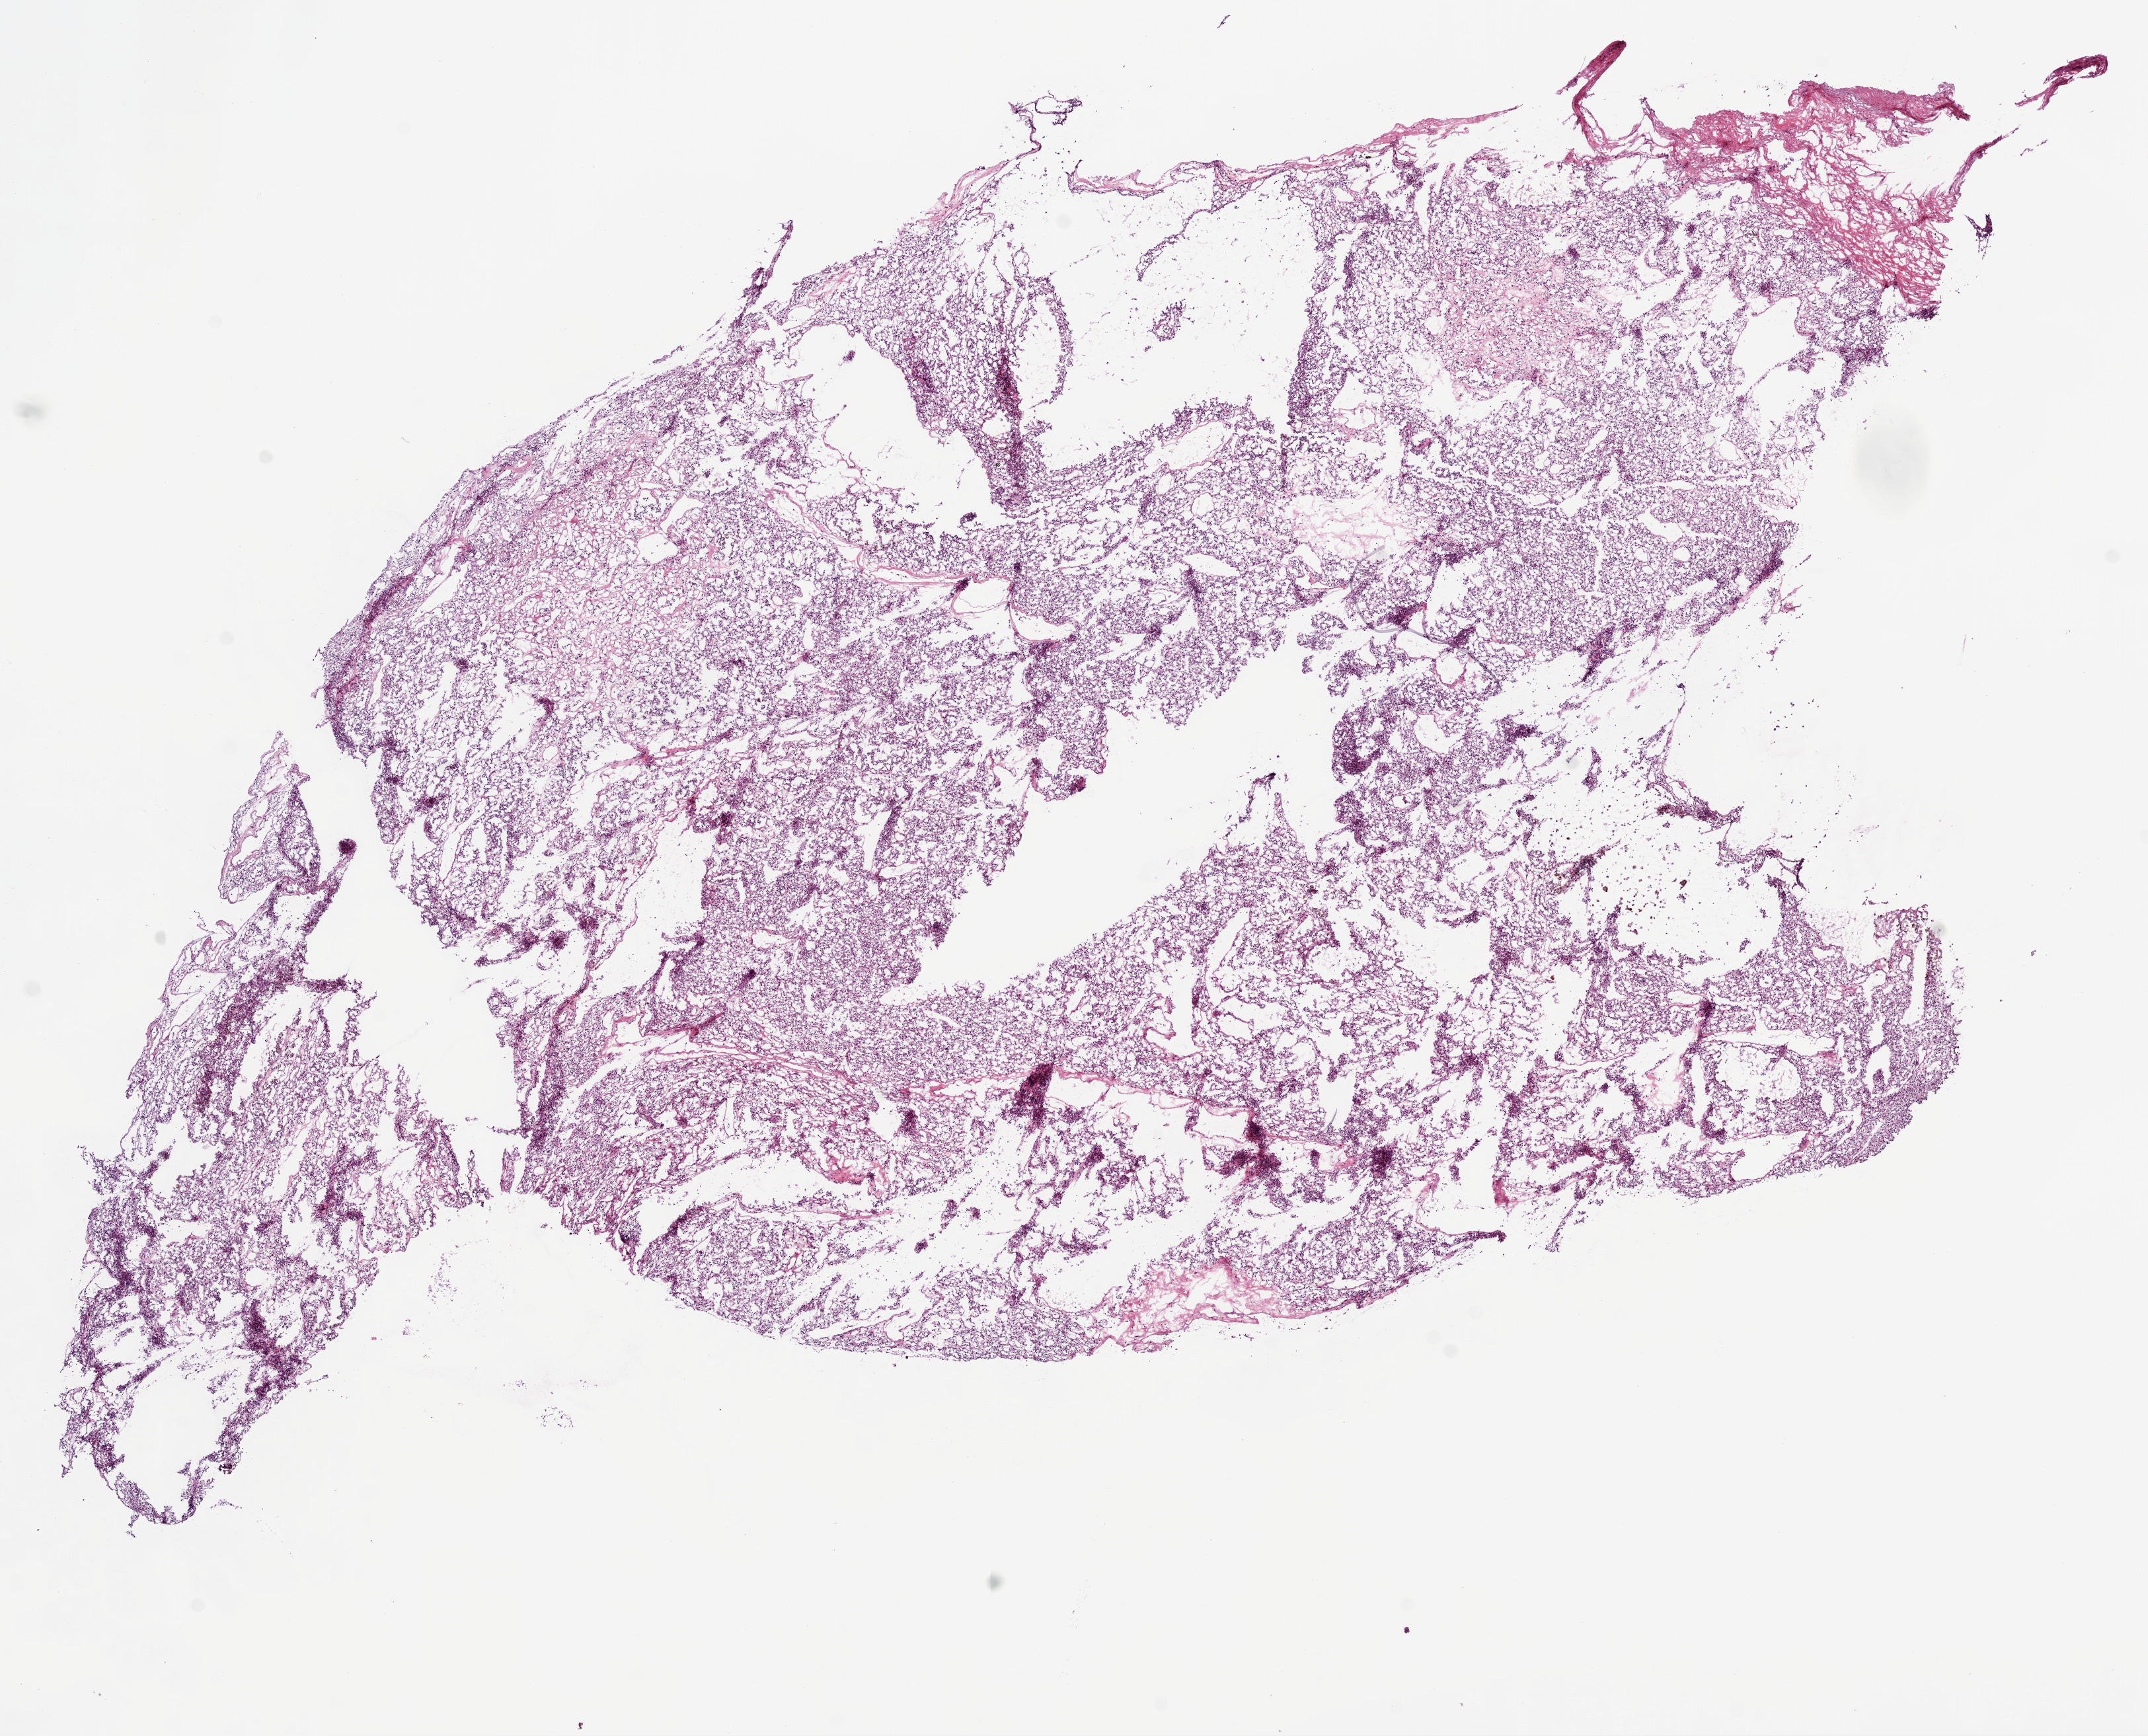
Digitized H&E tissue section (whole slide), whole scanned area (about 13.0 x 10.5 mm) shown as a low-resolution overview. Frozen section. Sample: primary tumour, kidney. Patient: male, age at initial diagnosis 59 years. Histologic grade: G2 (moderately differentiated). Composition of this section per pathologist review: tumour cells 90%, tumour nuclei 90%, normal cells 5%, stromal cells 5%, necrosis 0%.
Laterality: right. AJCC pathologic stage: I. Histologic diagnosis: Clear cell adenocarcinoma, NOS.